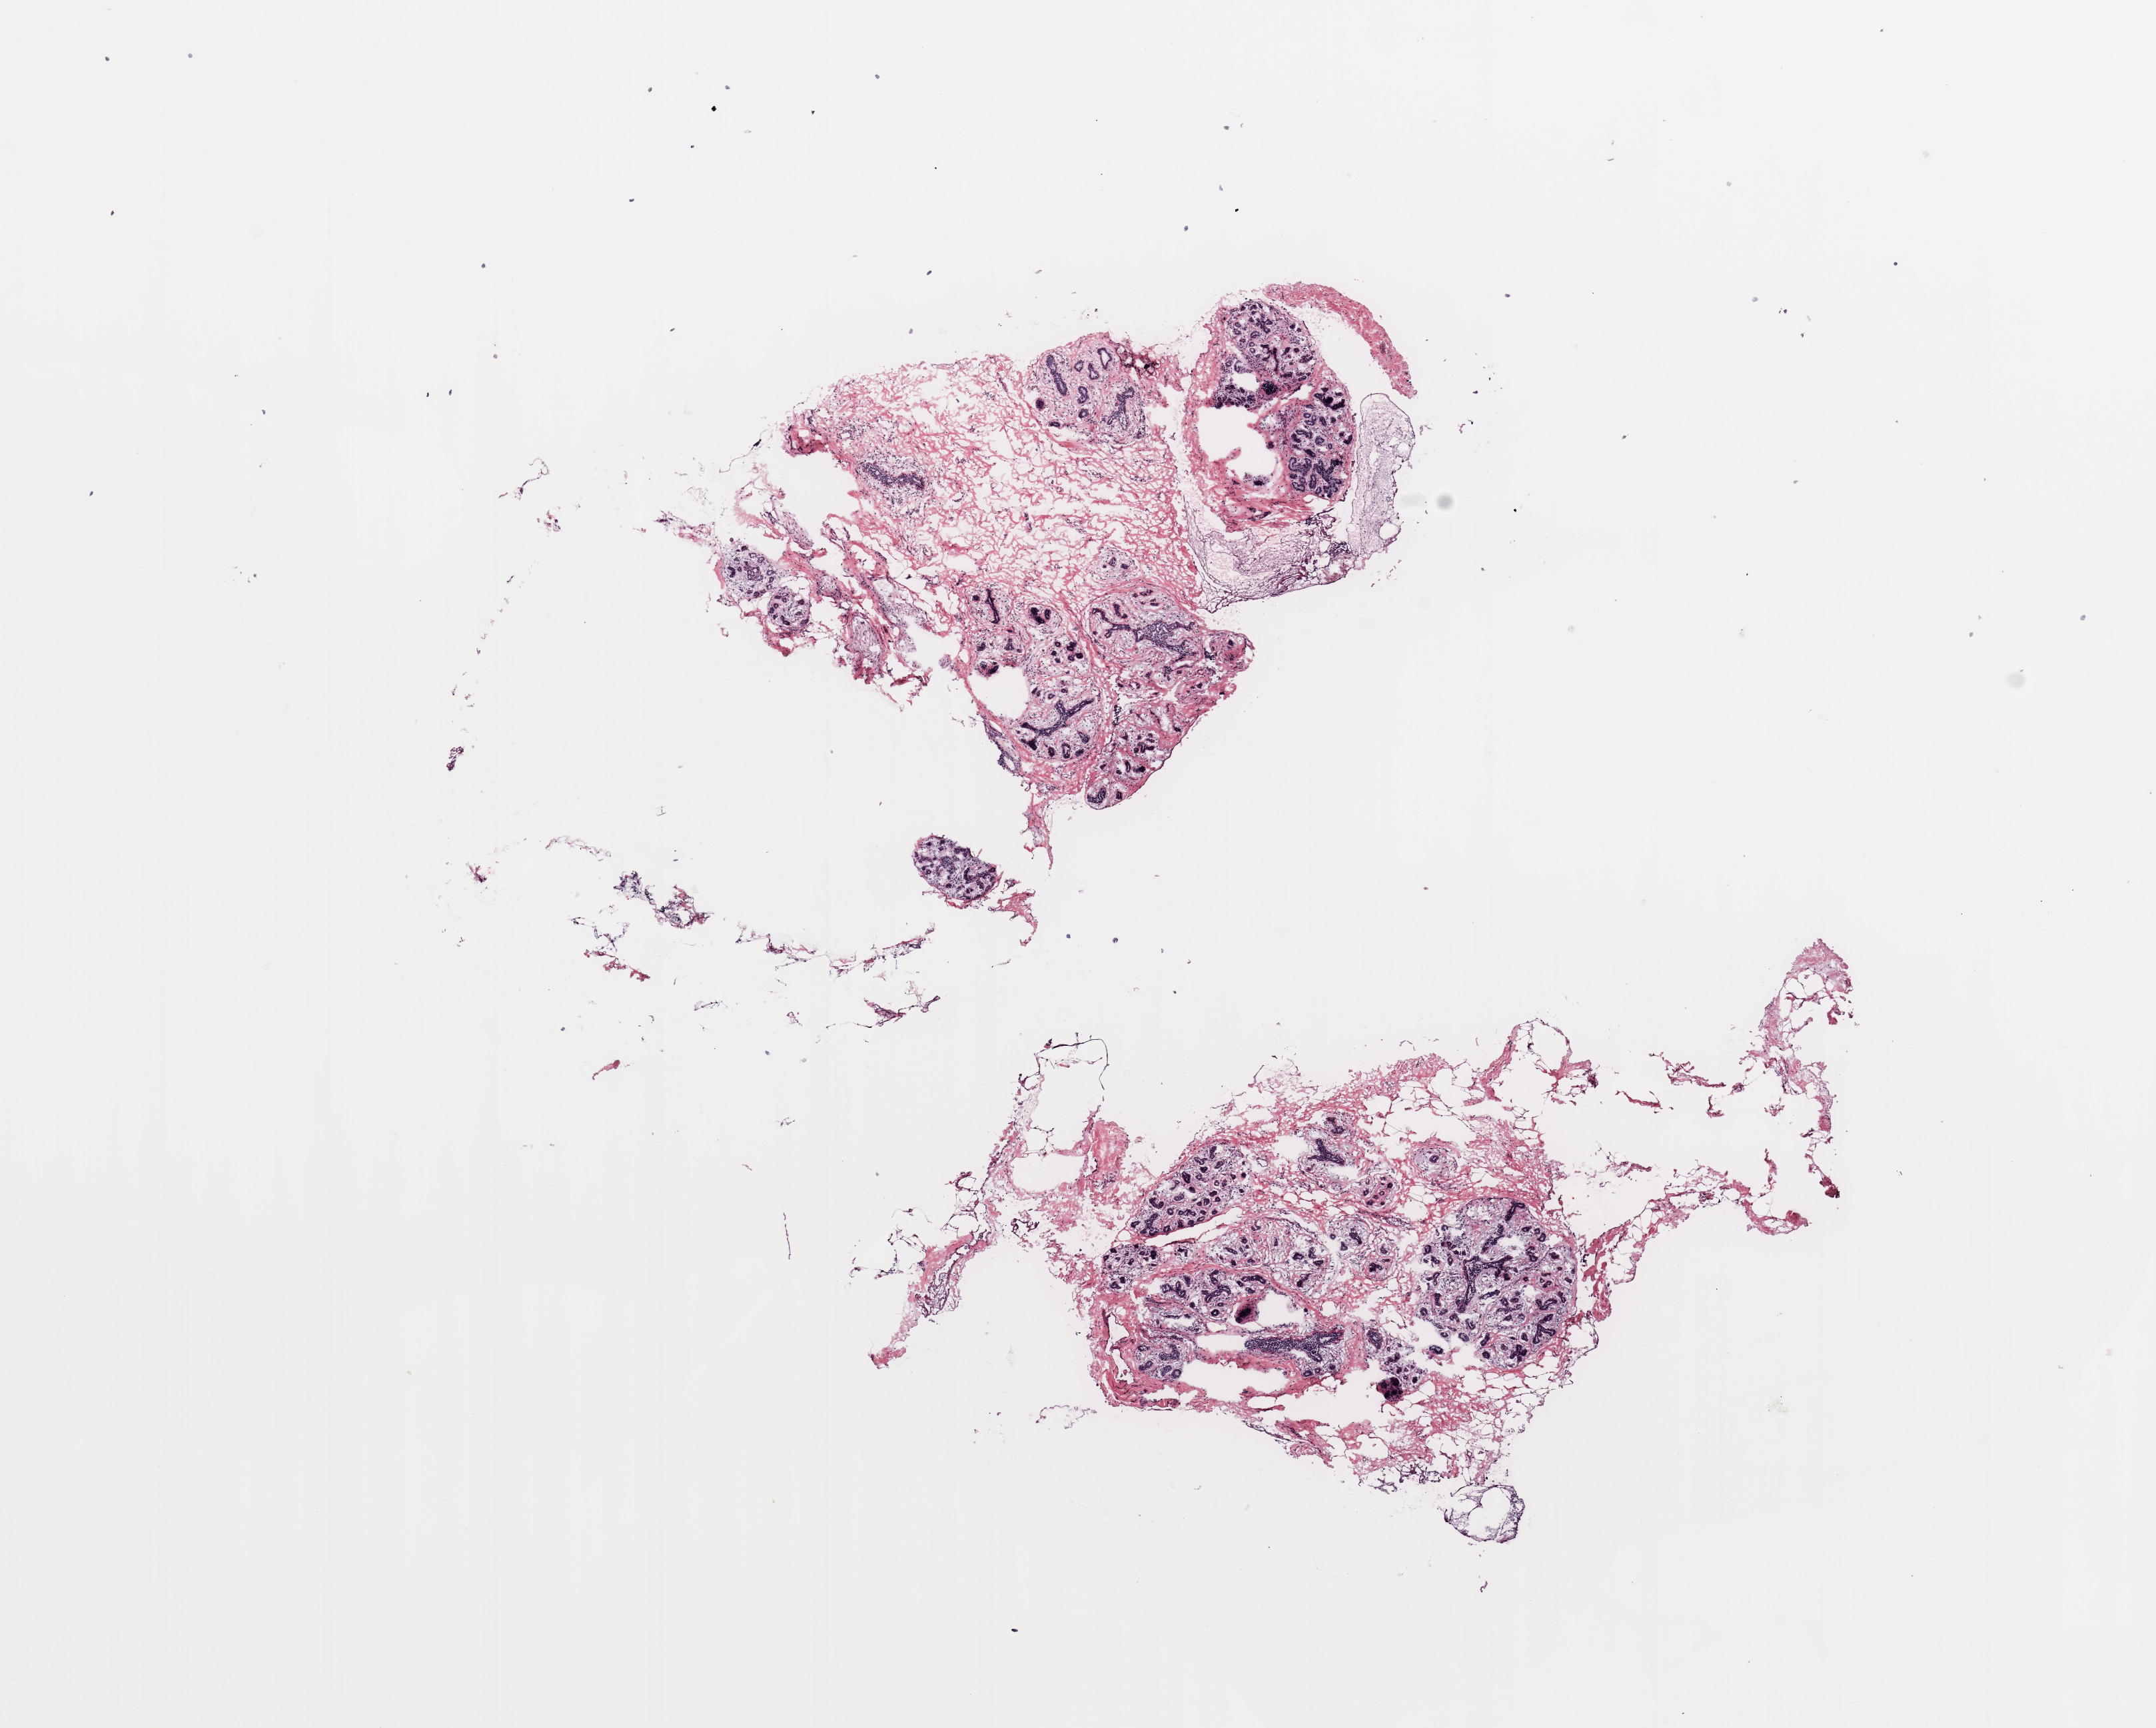
Whole-slide histology image, Hematoxylin and eosin (H&E) stained, whole scanned area (about 12.8 x 10.3 mm) shown as a low-resolution overview. Breast, tissue type not recorded.
- patient diagnosis (cohort enrolment): breast cancer (breast)